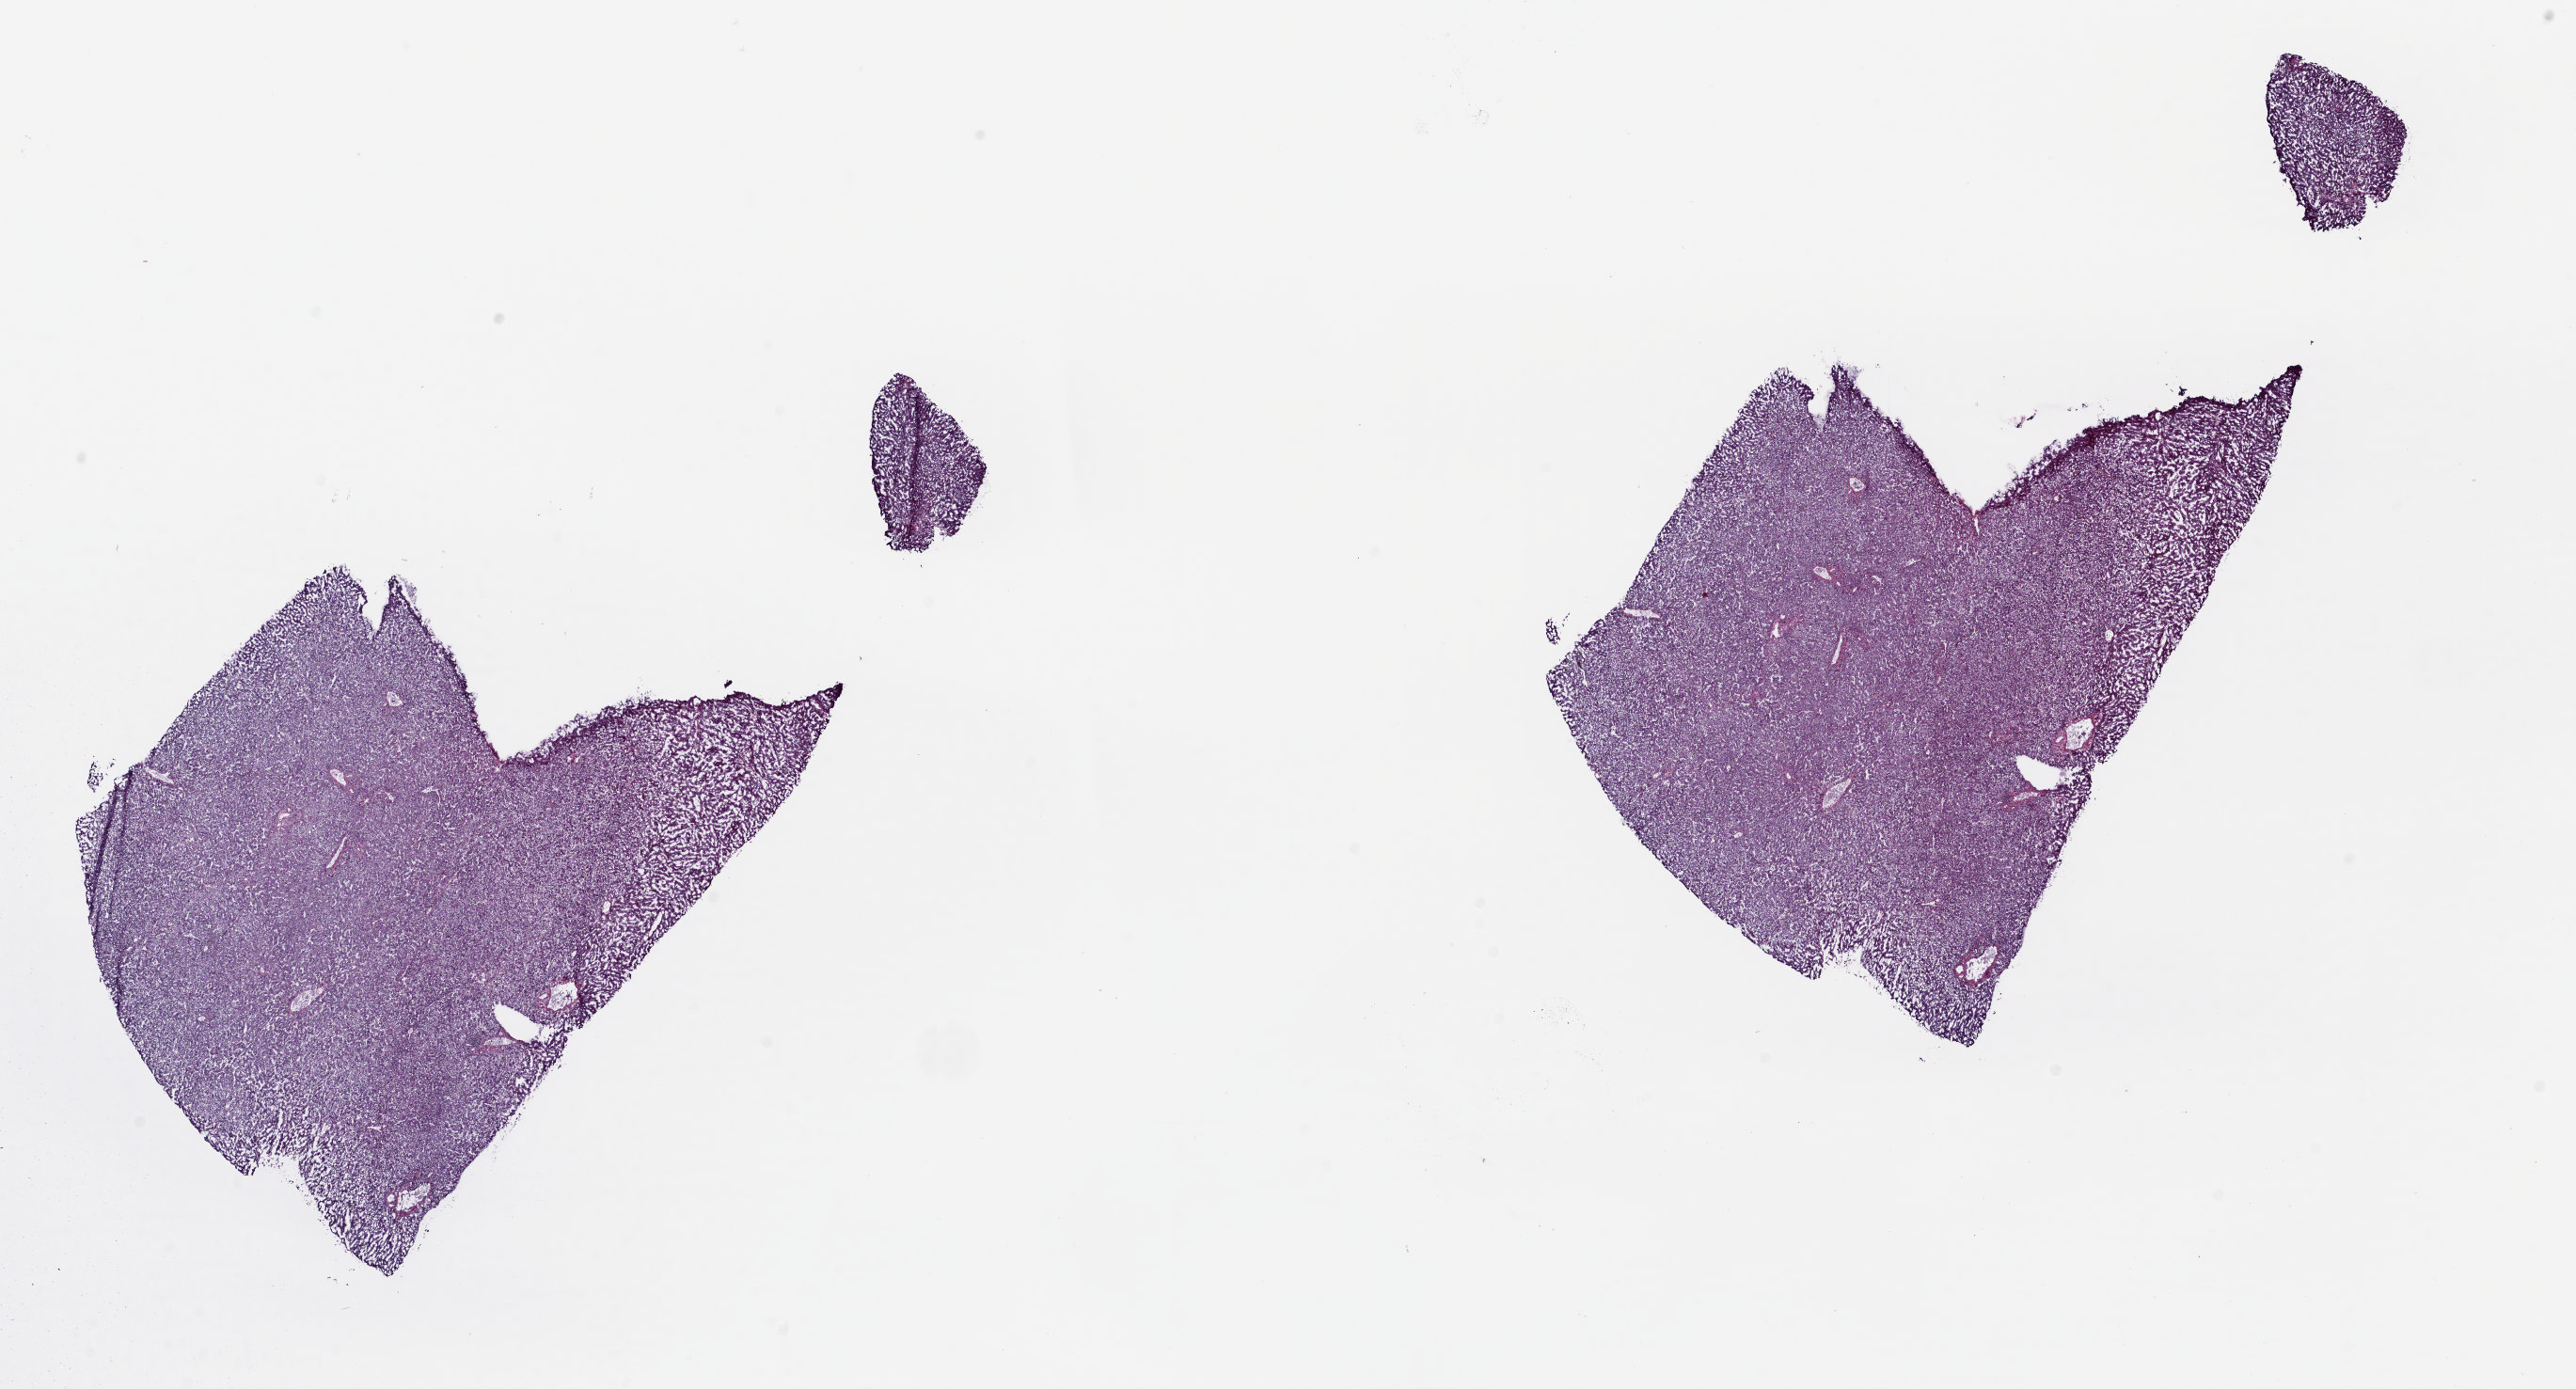
Whole-slide histology image, H&E-stained — low-resolution overview of the scanned area, about 21.8 x 11.7 mm (slide scanned at 20x); frozen section from the top of the tissue portion; solid tissue normal (non-tumour tissue) sample from the liver. Male, age 76 years at initial diagnosis. Pathologist review of this section (percent, as recorded): tumour cells 0%, tumour nuclei 0%, normal cells 100%, stromal cells 0%, necrosis 0%. Infiltration values recorded for this section: lymphocyte infiltration 0%, monocyte infiltration 0%, neutrophil infiltration 0%.
This section: solid tissue normal (non-tumour) sample from the same patient. Patient diagnosis: Hepatocellular carcinoma, NOS.